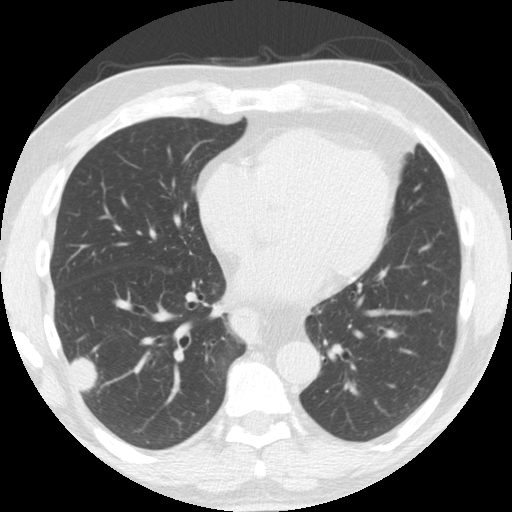
Low-dose screening chest CT, axial slice. Second annual screen. Lung window (W 1500 / L -600 HU). 2.5 mm slice thickness. 120 kVp. 512 × 512 image matrix, field of view 341 × 341 mm. Male participant, aged 61 years at enrolment. Former smoker at enrolment.
• Expert reader's lesion annotation, box from (x=44, y=321) to (x=112, y=398) px.
• Reader record for this screening exam (exam-level; its link to the box is not recorded): non-calcified nodule or mass ≥4 mm, right lower lobe, 33 × 19 mm, smooth margins, soft tissue attenuation, pre-existing on the prior screen: yes; interval growth: yes.
• Lung cancer was diagnosed 30 days after this screen: adenosquamous carcinoma, right lower lobe, poorly differentiated (G3), stage IV (AJCC 6th edition), 45 mm at pathology.